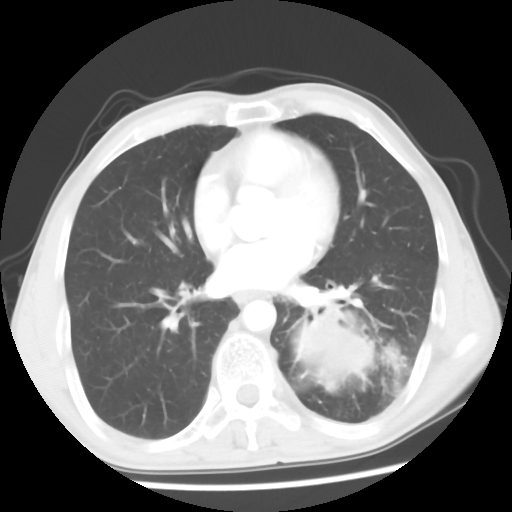
Chest CT, one axial slice; slice 25 of 56 in the series (ordered by position); reconstruction kernel STANDARD; lung window (W 1500 / L -600 HU); 512 × 512 image matrix. Male patient, age 60 years. Case-level facts recorded for this patient, not image findings: clinical TNM (as recorded): T4 N0 M0.
Structures marked on this image (rectangle marked by the reading radiologist):
- lung tumour (recorded histology: squamous cell carcinoma): bounding box (x1, y1, x2, y2) in pixels: (291, 302, 411, 420)